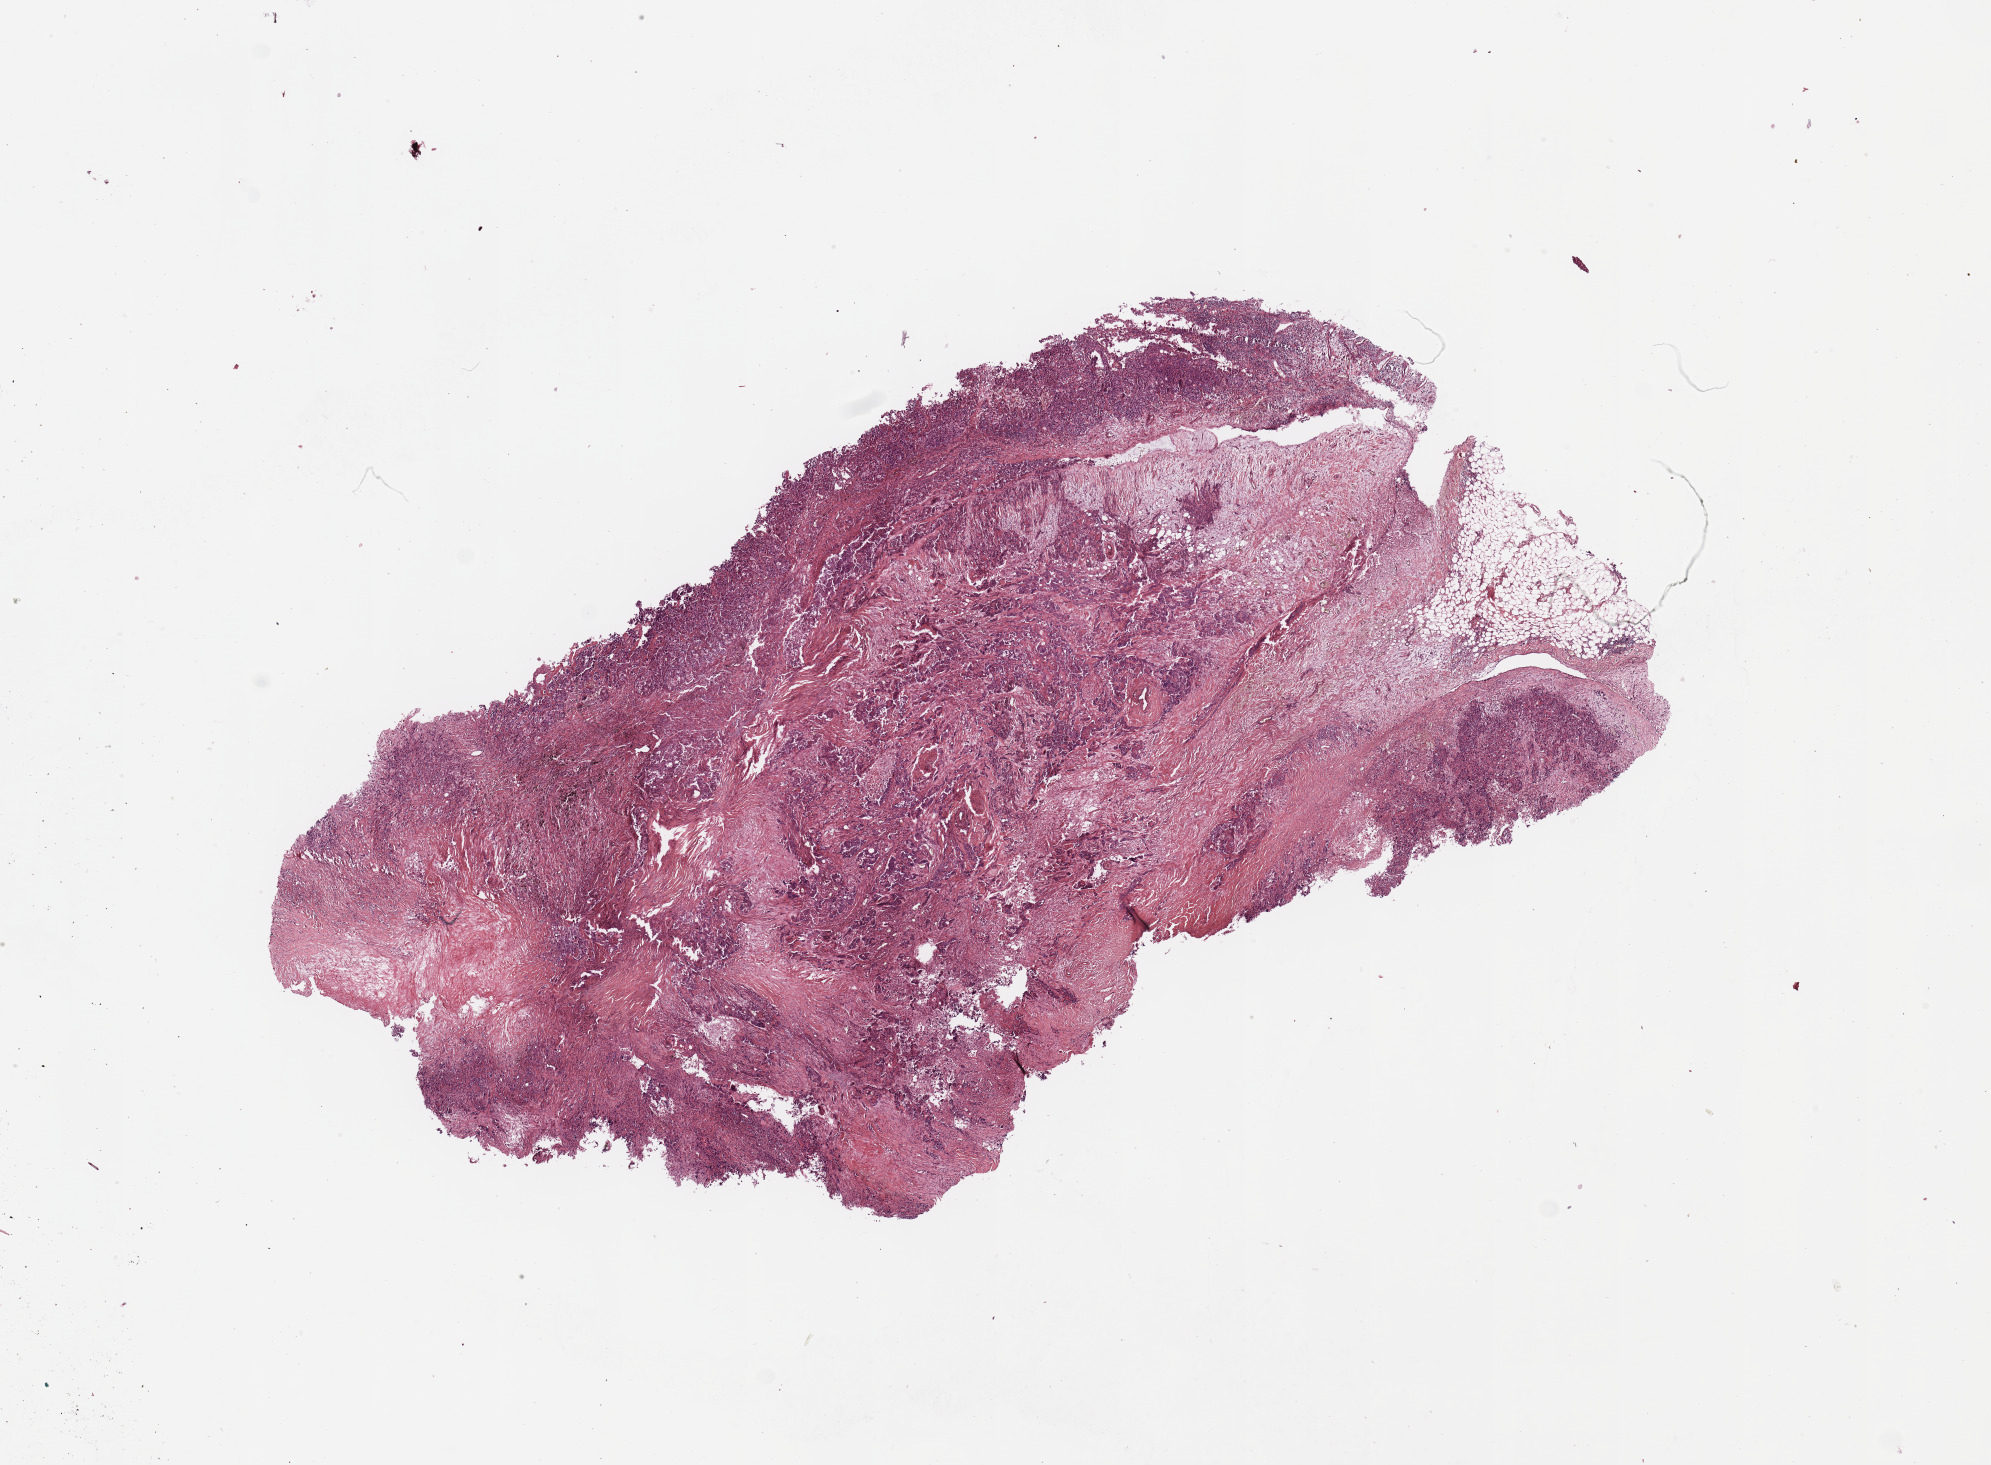
Digitized Hematoxylin and eosin (H&E) stained tissue section (whole slide), a low-resolution overview of the entire scanned area, about 15.8 x 11.6 mm. Tumour tissue sample, lung. Patient: male, age 70 years. Histologic grade: G2 (moderately differentiated).
AJCC pathologic stage: IB. Diagnosis: Squamous cell carcinoma, NOS. Primary tumour site (as recorded): right middle lobe.